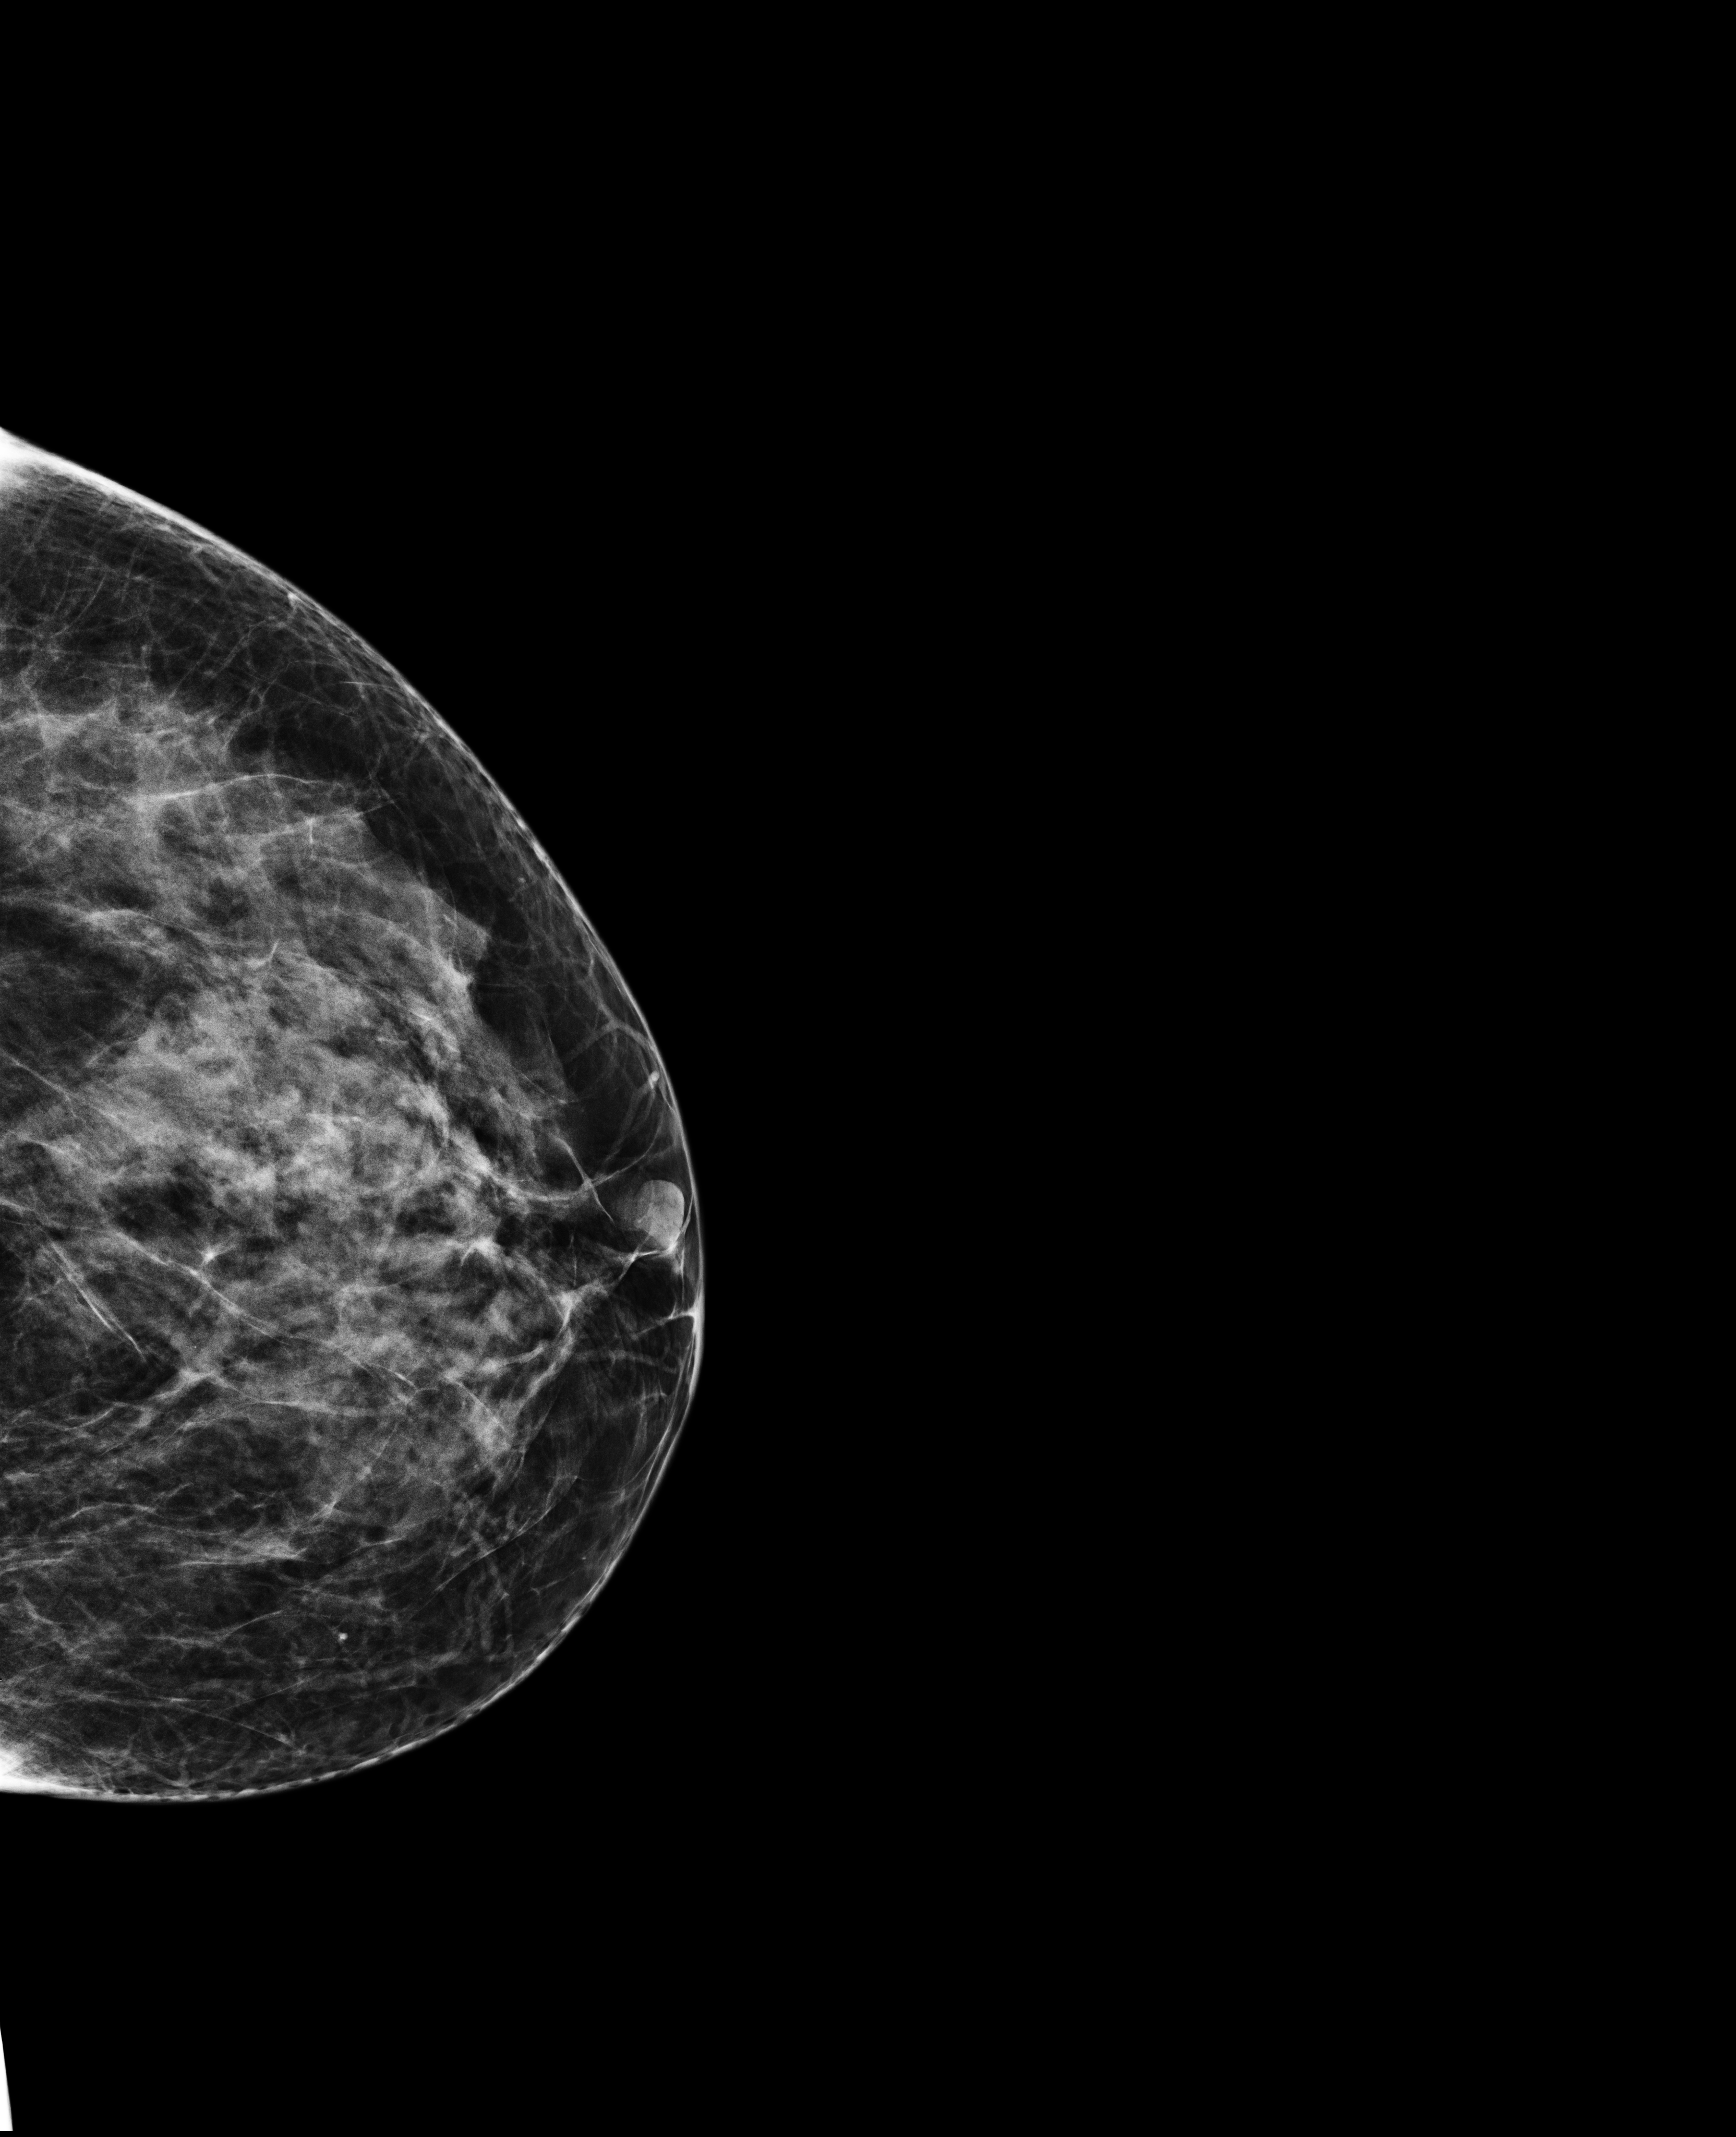
Digital mammogram (FFDM); right breast; craniocaudal (CC) view; annual screening mammography examination; compressed breast thickness 55 mm. Female patient, age 48 years.
BI-RADS breast density category at the screening exam (both breasts, scale 1–4): 3. Final BI-RADS assessment for this screening round (tomosynthesis exam, both breasts): category 1. Recall: no recall after this screen.